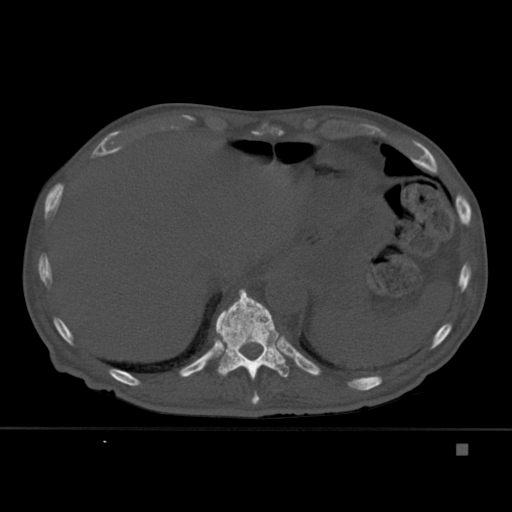
CT including the spine, one axial slice; position 219 of 451 along the scan axis; bone window (W 1800 / L 400 HU); 512 × 512 image matrix, field of view 378 × 378 mm. Male patient, age 75 years. From the clinical record (not read from this slice): primary cancer: prostate.
Structures marked on this image (semi-automatically segmented with operator editing):
- T10 vertebra: bounding box [x1, y1, x2, y2] px = [251, 374, 260, 405]
- T11 vertebra: [214, 289, 289, 381]